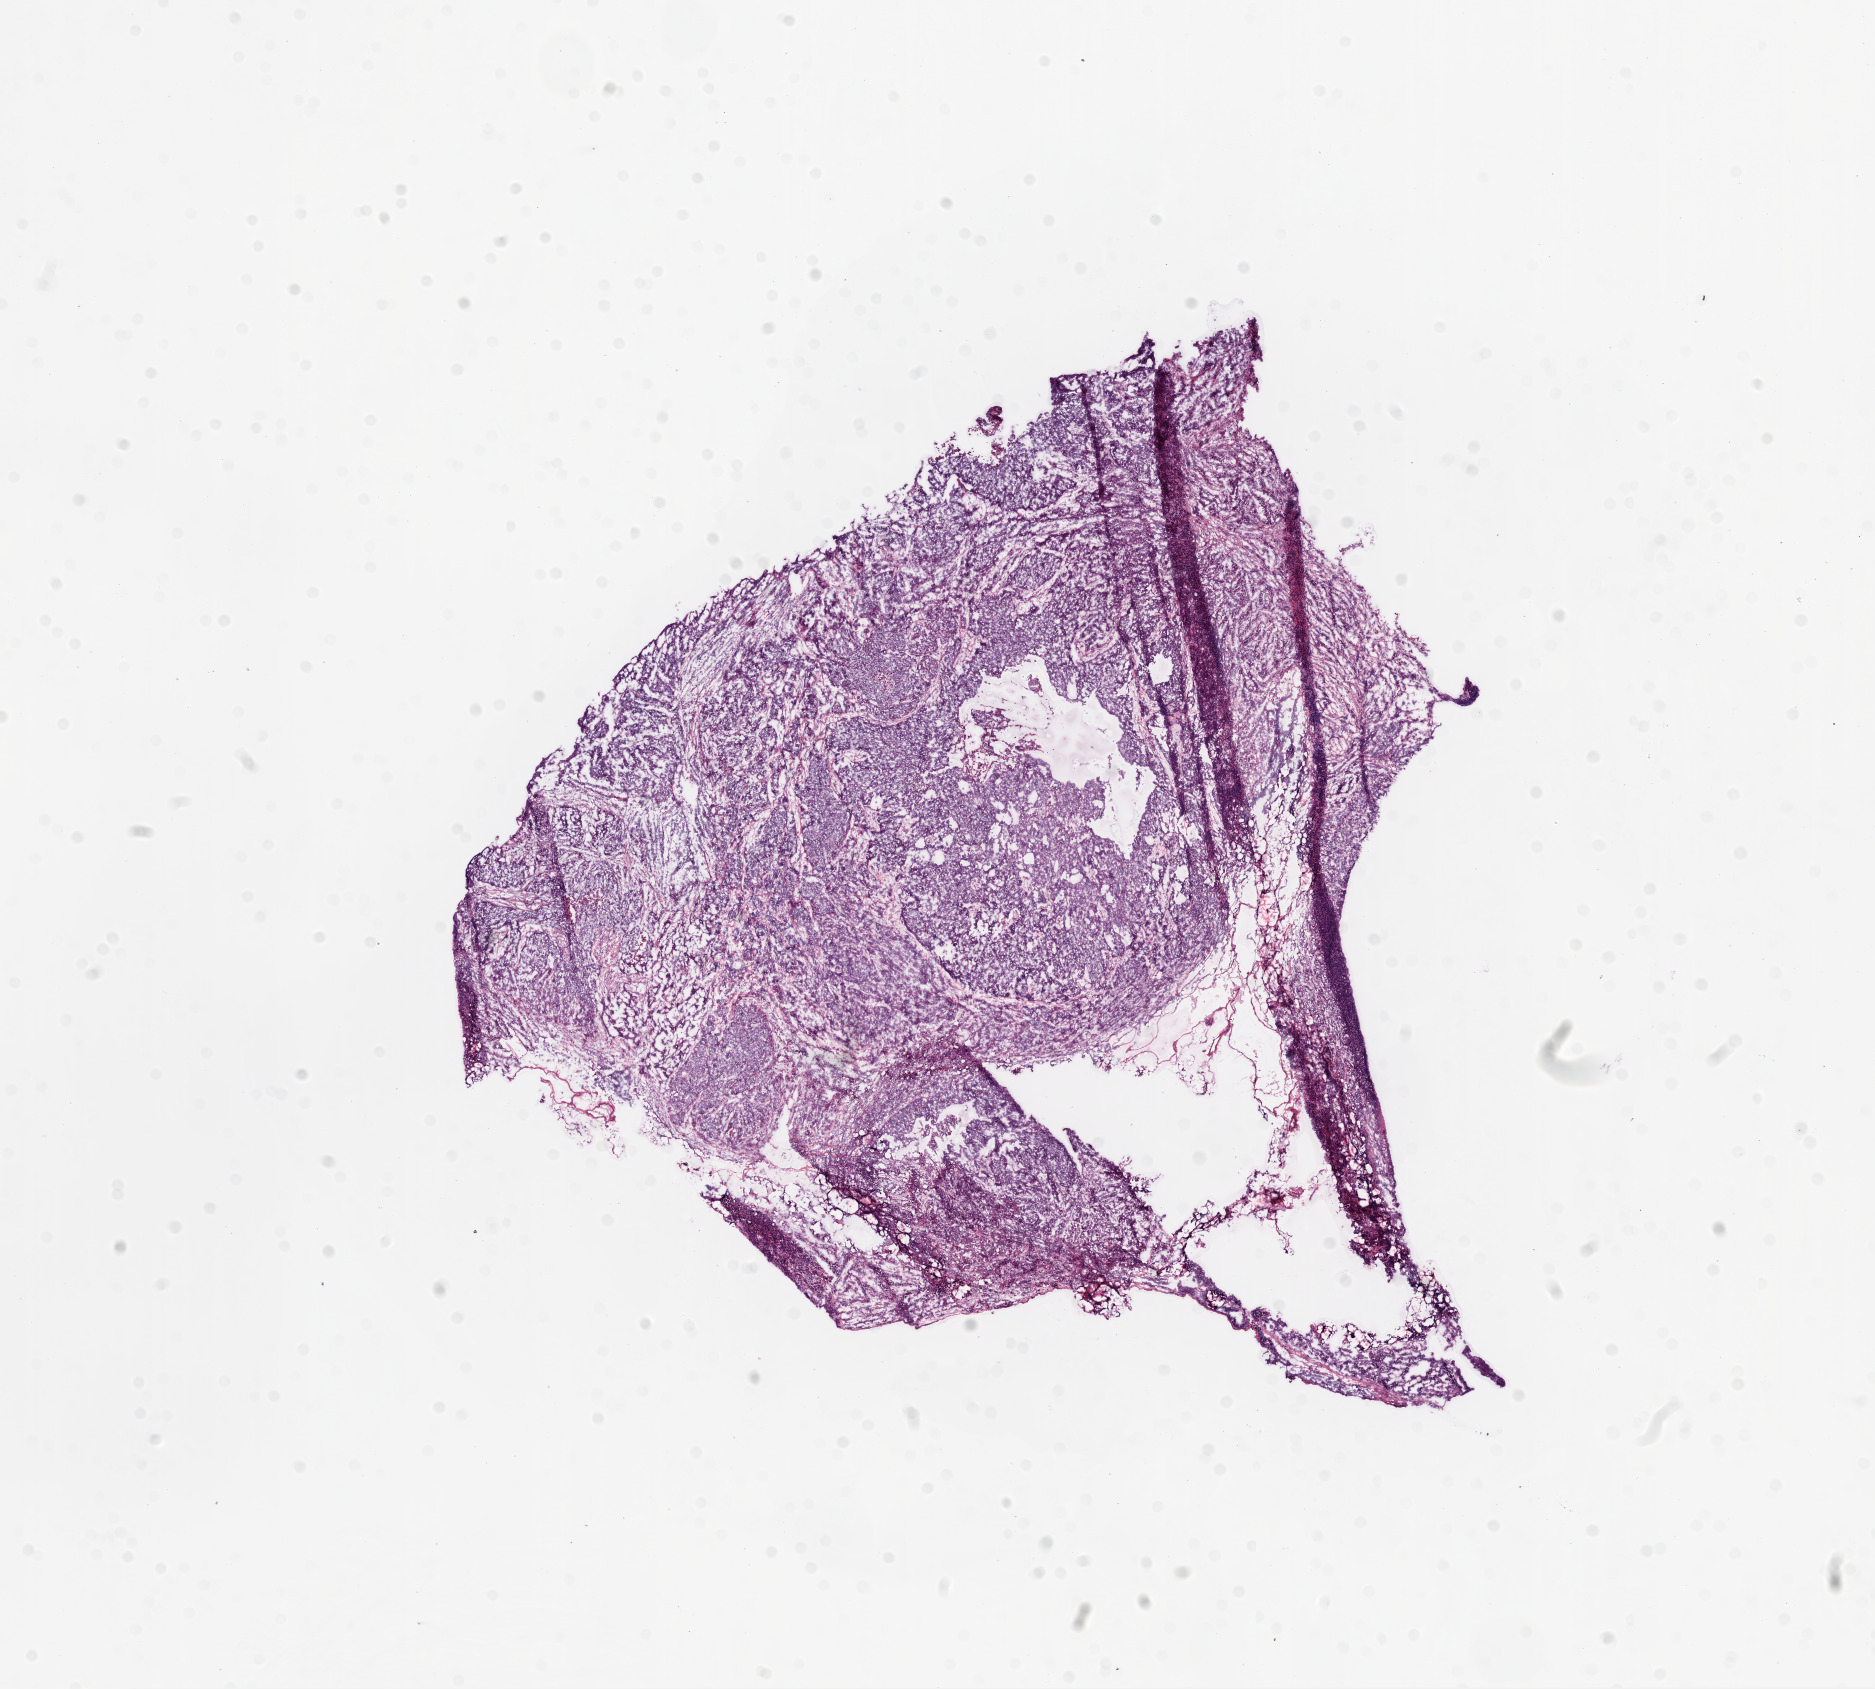
Whole-slide histology image, Hematoxylin and eosin (H&E) stained — shown as a low-resolution overview of the whole scanned area (about 15.0 x 13.6 mm). Frozen section. Ovary, primary tumour sample. Patient: female, age at initial diagnosis 70 years. Histologic grade: G3 (poorly differentiated). Slide review estimates, as recorded: tumour cells 85%, tumour nuclei 90%, normal cells 0%, stromal cells 10%, necrosis 5%.
* FIGO stage: IIIC
* pathologic diagnosis: Serous cystadenocarcinoma, NOS